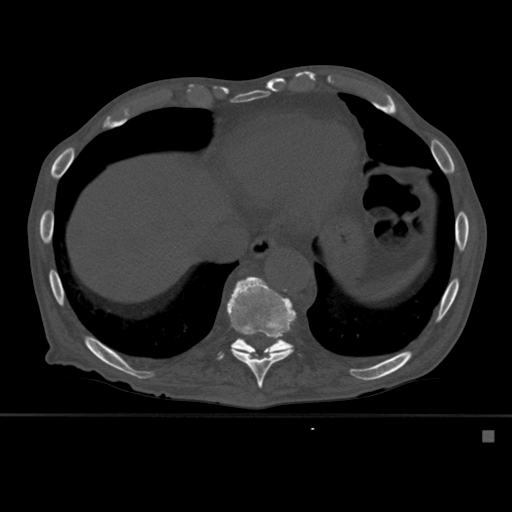
CT including the spine, one axial slice. Slice 309 of 527 in the series (ordered by position). Bone window (W 1800 / L 400 HU). 1.5 mm slice thickness. 512 × 512 image matrix, field of view 373 × 373 mm. Male patient, age 78 years. From the clinical record (not read from this slice): primary cancer: prostate.
Outlined on this slice (semi-automatically segmented with operator editing):
- T10 vertebra: bounding box <226,276,297,389> (left, top, right, bottom; pixels)
- T11 vertebra: <219,338,294,360>